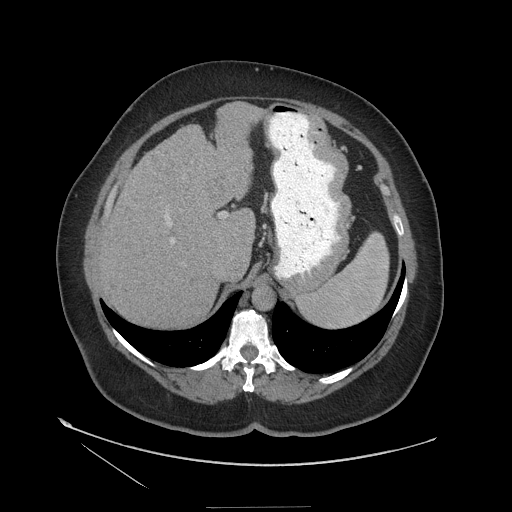
Contrast-enhanced abdominal CT (liver protocol), one axial slice. Slice 84 of 127 in the series (ordered by position). Soft-tissue window (W 400 / L 40 HU). 2.5 mm slice thickness. 512 × 512 image matrix, field of view 480 × 480 mm. Case-level facts recorded for this patient, not image findings: diagnosis: hepatocellular carcinoma (patient treated with transarterial chemoembolisation; whether this scan precedes or follows treatment is not stated here); TNM stage (as recorded): Stage-II; Child-Pugh class: A; tumour differentiation: well differentiated; tumour nodularity: multinodular.
Outlined on this slice (semi-automatic segmentation, software-assisted and operator-edited):
- liver parenchyma outside the tumour (the mass and vessels are separate outlines, so this box may not span the whole liver): bounding box <98,104,264,326> (left, top, right, bottom; pixels)
- mass: <123,235,140,253>
- liver vessels: <164,212,223,242>